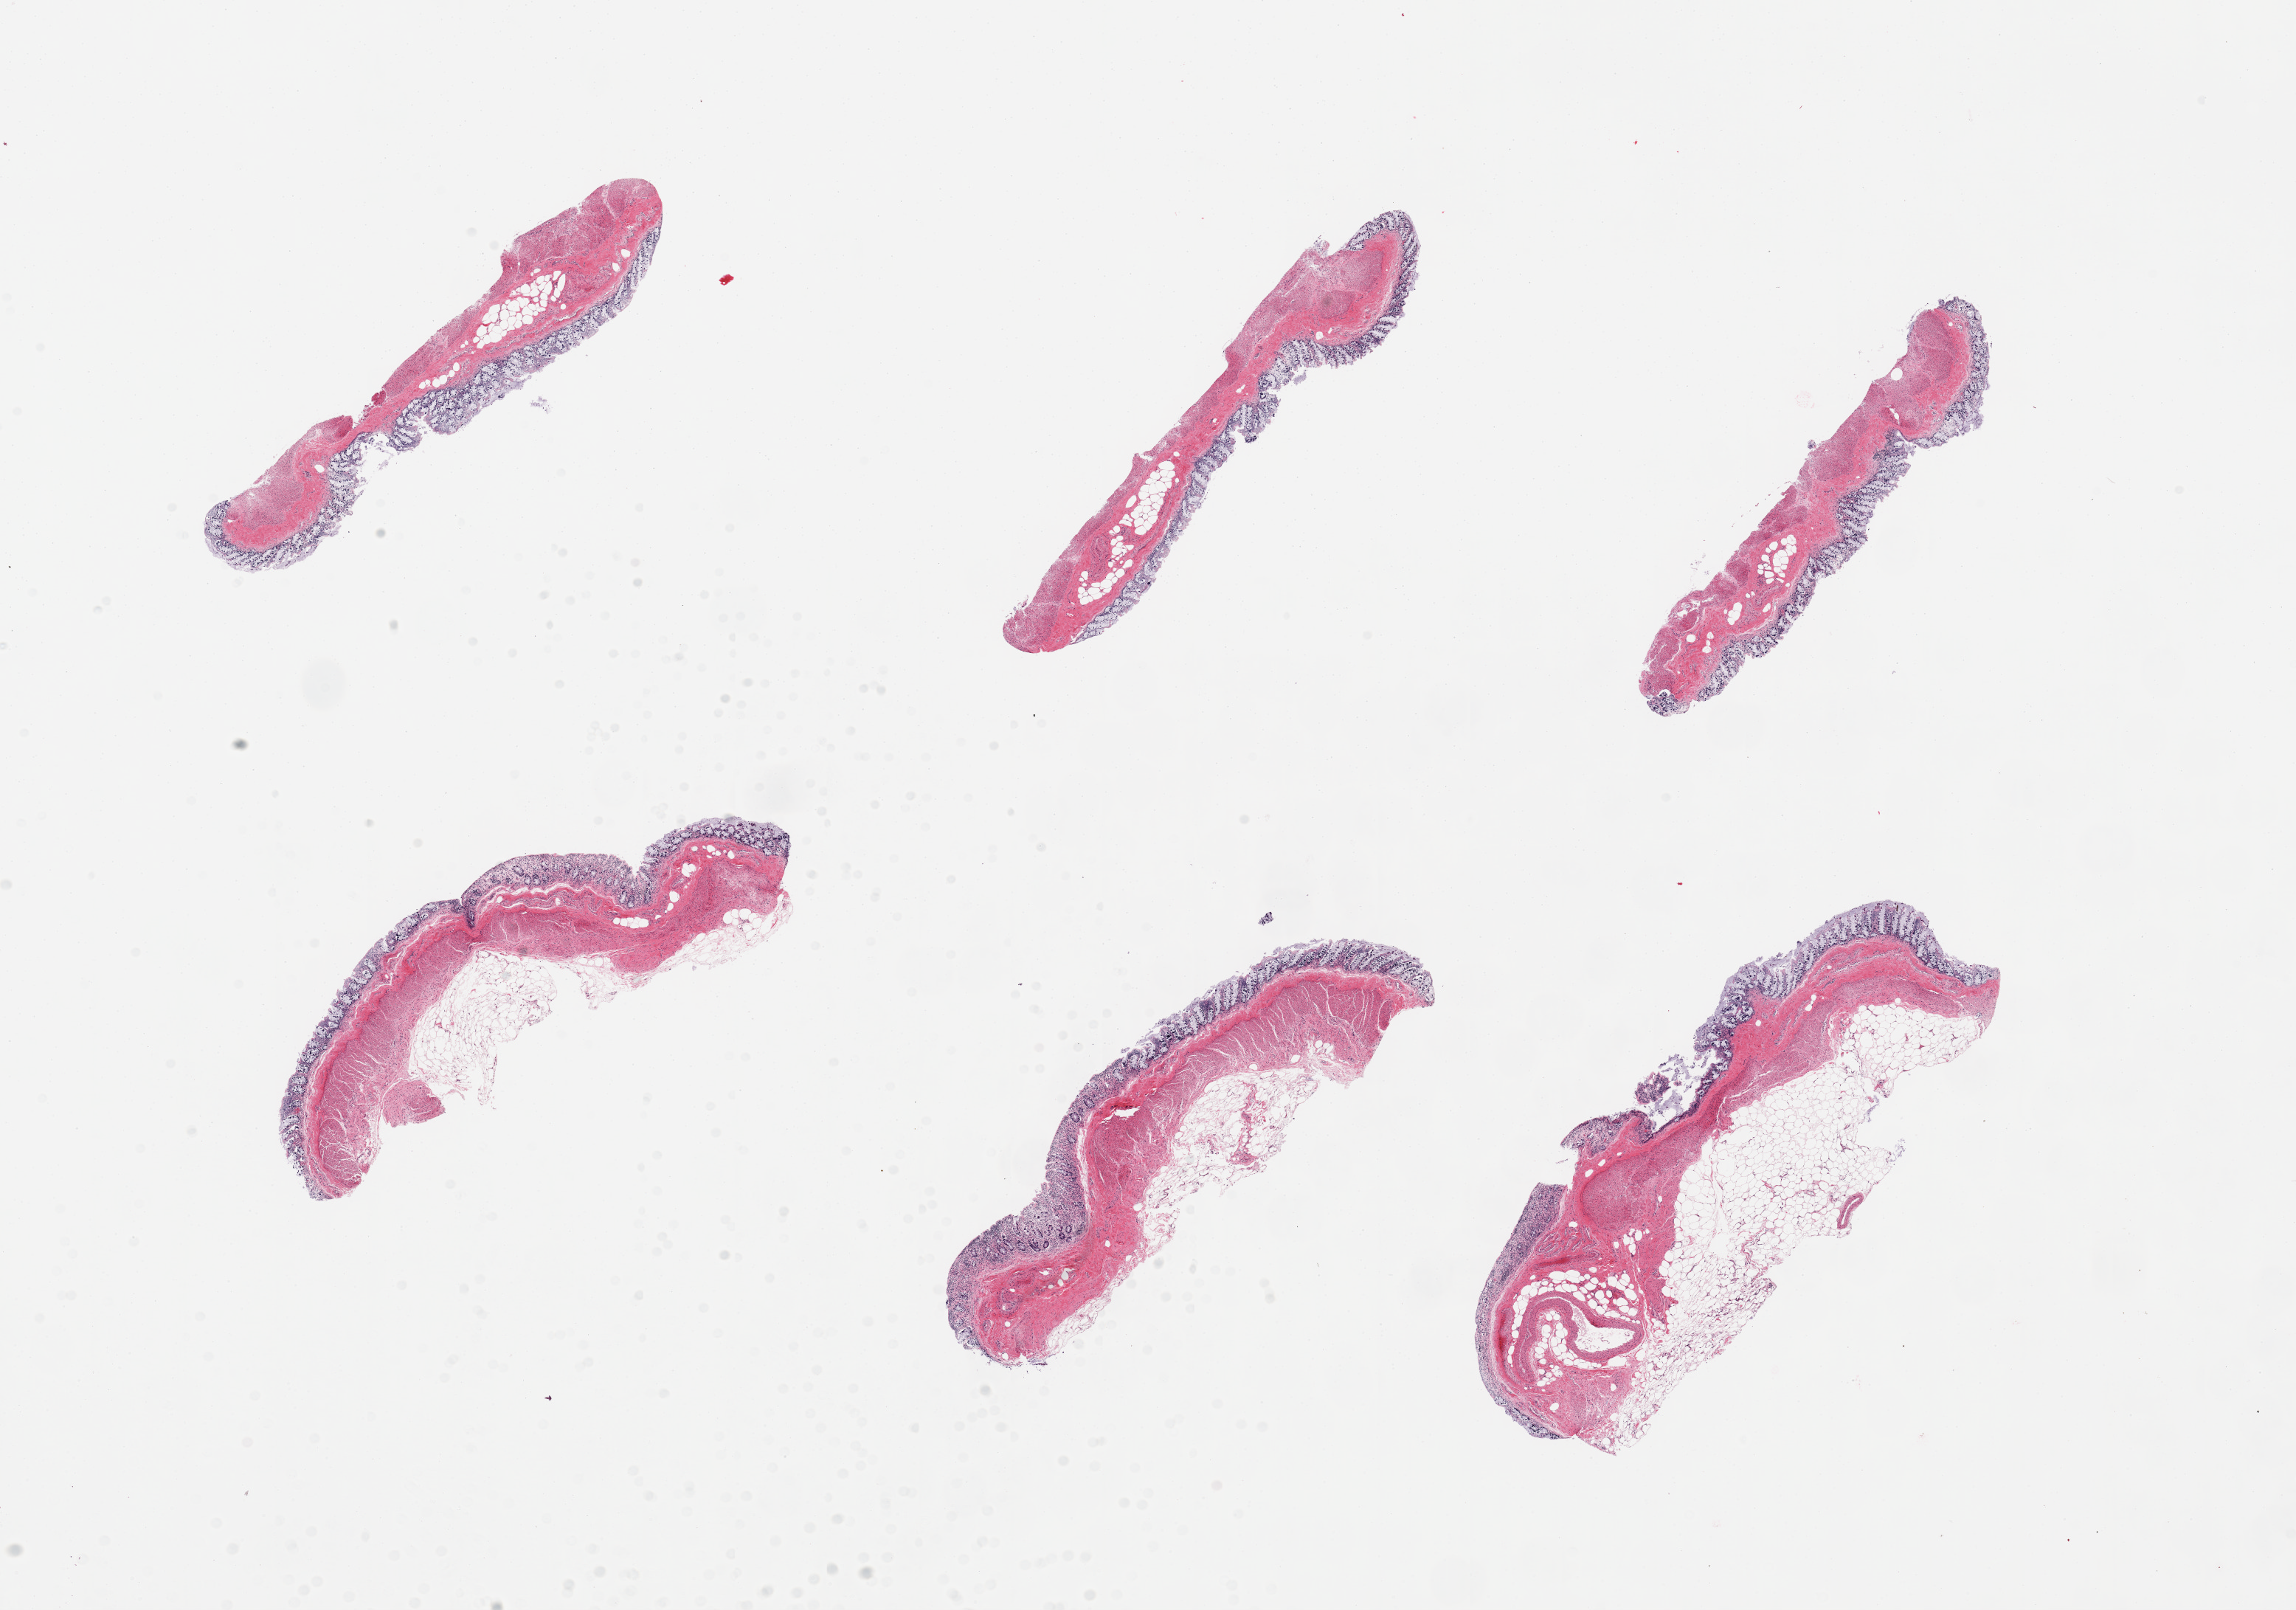
Digitized haematoxylin and eosin-stained section, shown as a low-resolution overview of the whole scanned area (about 24.6 x 17.3 mm, acquisition: 20x scan). PAXgene-fixed paraffin-embedded (PFPE) section. Section of transverse colon (target tissue). Donor tissue sample. Donor sex: male.
Pathologist's review note for this sample: 6 pieces, full thickness colon.